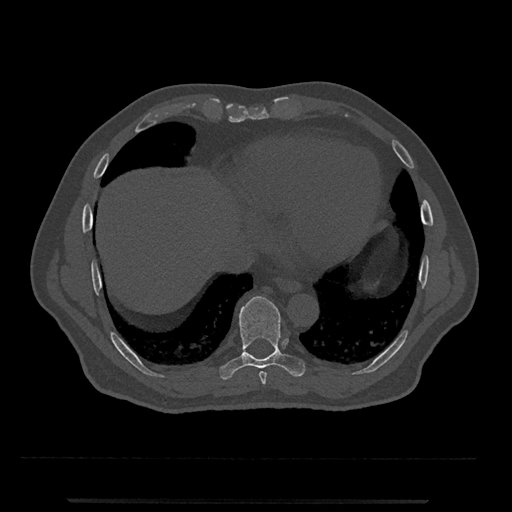
CT including the spine, one axial slice. Bone window (W 1800 / L 400 HU). 512 × 512 image matrix, field of view 419 × 419 mm. Male patient, age 63 years. From the clinical record (not read from this slice): primary cancer: prostate.
Annotated regions visible in this slice (semi-automatic segmentation, software-assisted and operator-edited):
- T8 vertebra: bounding box (x1, y1, x2, y2) in pixels: (259, 371, 267, 385)
- T9 vertebra: (219, 296, 306, 380)